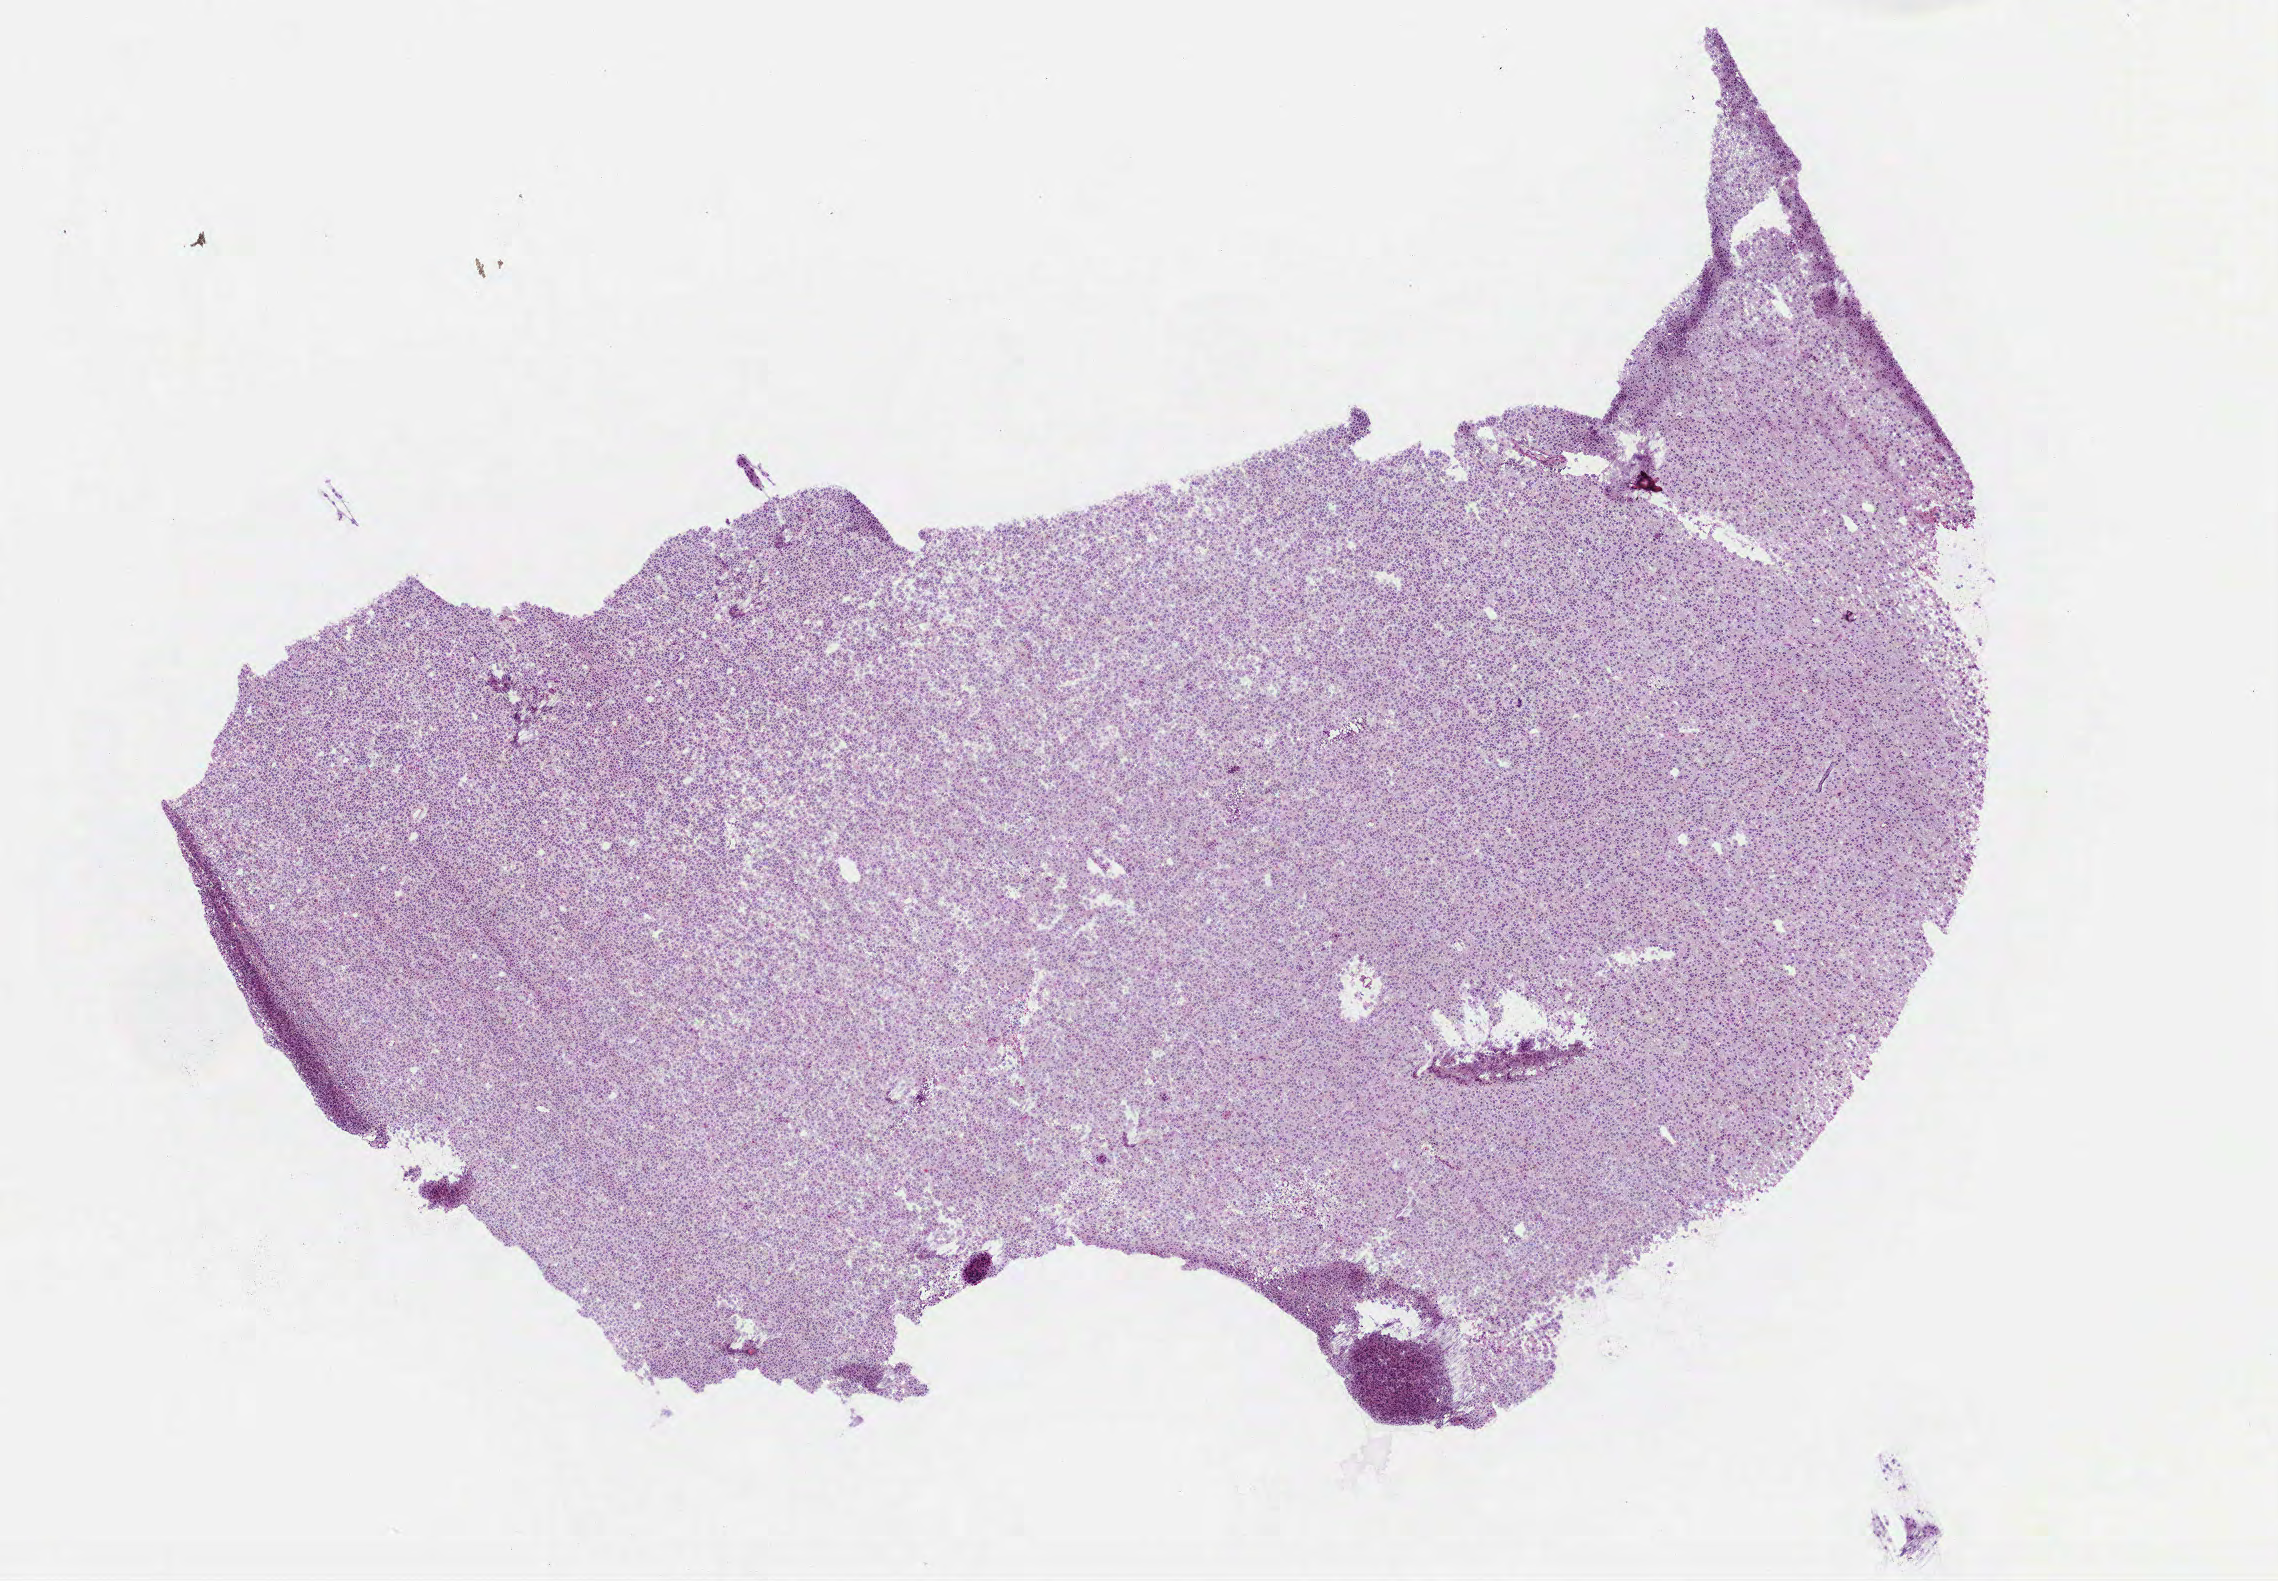
Whole-slide histology image, H&E-stained — whole scanned area (about 9.2 x 6.4 mm) shown as a low-resolution overview, frozen section, primary tumour sample from the brain. Female, age 47 years at initial diagnosis. Slide review estimates, as recorded: tumour cells 100%, tumour nuclei 85%.
Histologic diagnosis: Oligodendroglioma, NOS (cerebrum).